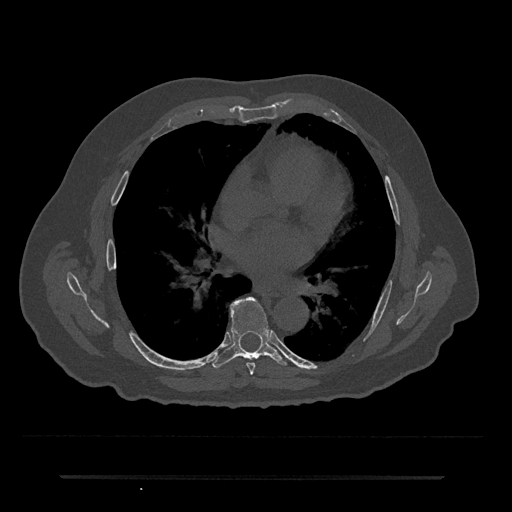
CT including the spine, one axial slice; slice 402 of 797 in the series (ordered by position); 120 kVp; bone window (W 1800 / L 400 HU); 0.5 mm slice thickness; 512 × 512 image matrix, field of view 437 × 437 mm. Male patient, age 69 years. From the clinical record (not read from this slice): primary cancer: prostate.
Outlined on this slice (semi-automatic segmentation, software-assisted and operator-edited):
- T6 vertebra: bounding box <246,363,255,375> (left, top, right, bottom; pixels)
- T7 vertebra: <212,297,287,368>